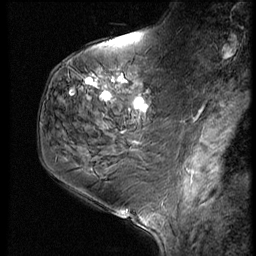
Breast MRI (dynamic contrast-enhanced), one sagittal slice; position 25 of 60 along the scan axis; 3 images stored at this slice position (order not interpretable as contrast timing); 1.5 T; TE 4.2 ms, TR 9 ms; 2.5 mm slice thickness; 256 × 256 image matrix, field of view 180 × 180 mm. Female patient, age 59 years. From the clinical record (not read from this slice): setting: breast cancer imaged before/during neoadjuvant chemotherapy; receptor status: HER2-positive.
Outlined on this slice (semi-automatic segmentation, software-assisted and operator-edited):
- analysis volume of interest (the breast-tissue region the enhancement analysis was run in; not a lesion): bounding box [x1, y1, x2, y2] px = [78, 61, 161, 125]
- tumour enhancement mask (voxels above the 140 % enhancement threshold inside the analysis volume of interest): [86, 79, 146, 108]